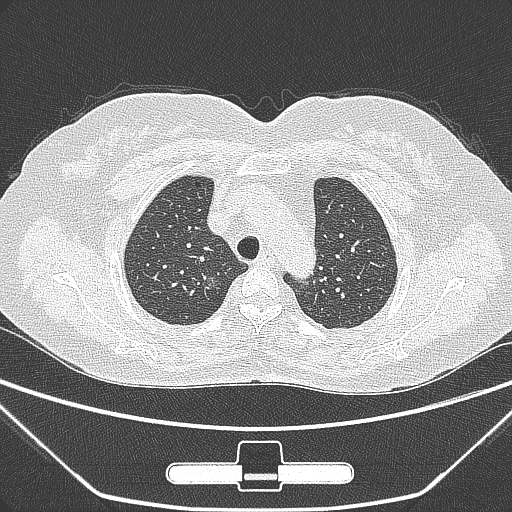
Chest CT, one axial slice; slice 223 of 275 in the series (ordered by position); 120 kVp; lung window (W 1500 / L -600 HU); 512 × 512 image matrix, field of view 356 × 356 mm. Patient: female, 63 years. Case-level facts recorded for this patient, not image findings: clinical TNM (as recorded): T1a N0 M0.
Outlined on this slice (rectangle marked by the reading radiologist):
- lung tumour (recorded histology: adenocarcinoma): bounding box <197,264,224,298> (left, top, right, bottom; pixels)